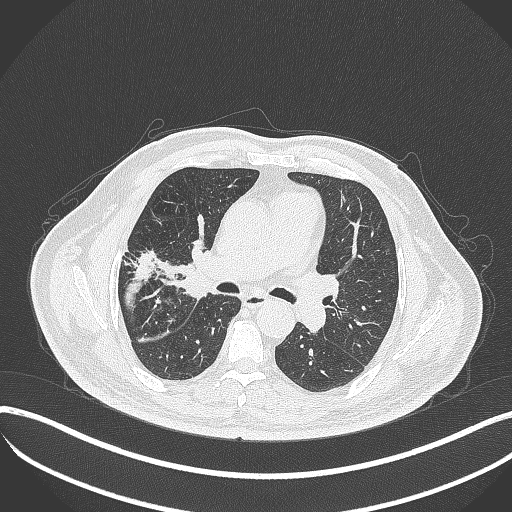
Chest CT, one axial slice; position 212 of 401 along the scan axis; reconstruction kernel B70f; 120 kVp; lung window (W 1500 / L -600 HU); 1 mm slice thickness; 512 × 512 image matrix, field of view 400 × 400 mm. Male patient, age 72 years. Case-level facts recorded for this patient, not image findings: clinical TNM (as recorded): T1c N0 M0.
Outlined on this slice (bounding box drawn by a radiologist):
- lung tumour (recorded histology: squamous cell carcinoma): bounding box [x1, y1, x2, y2] px = [170, 242, 215, 307]